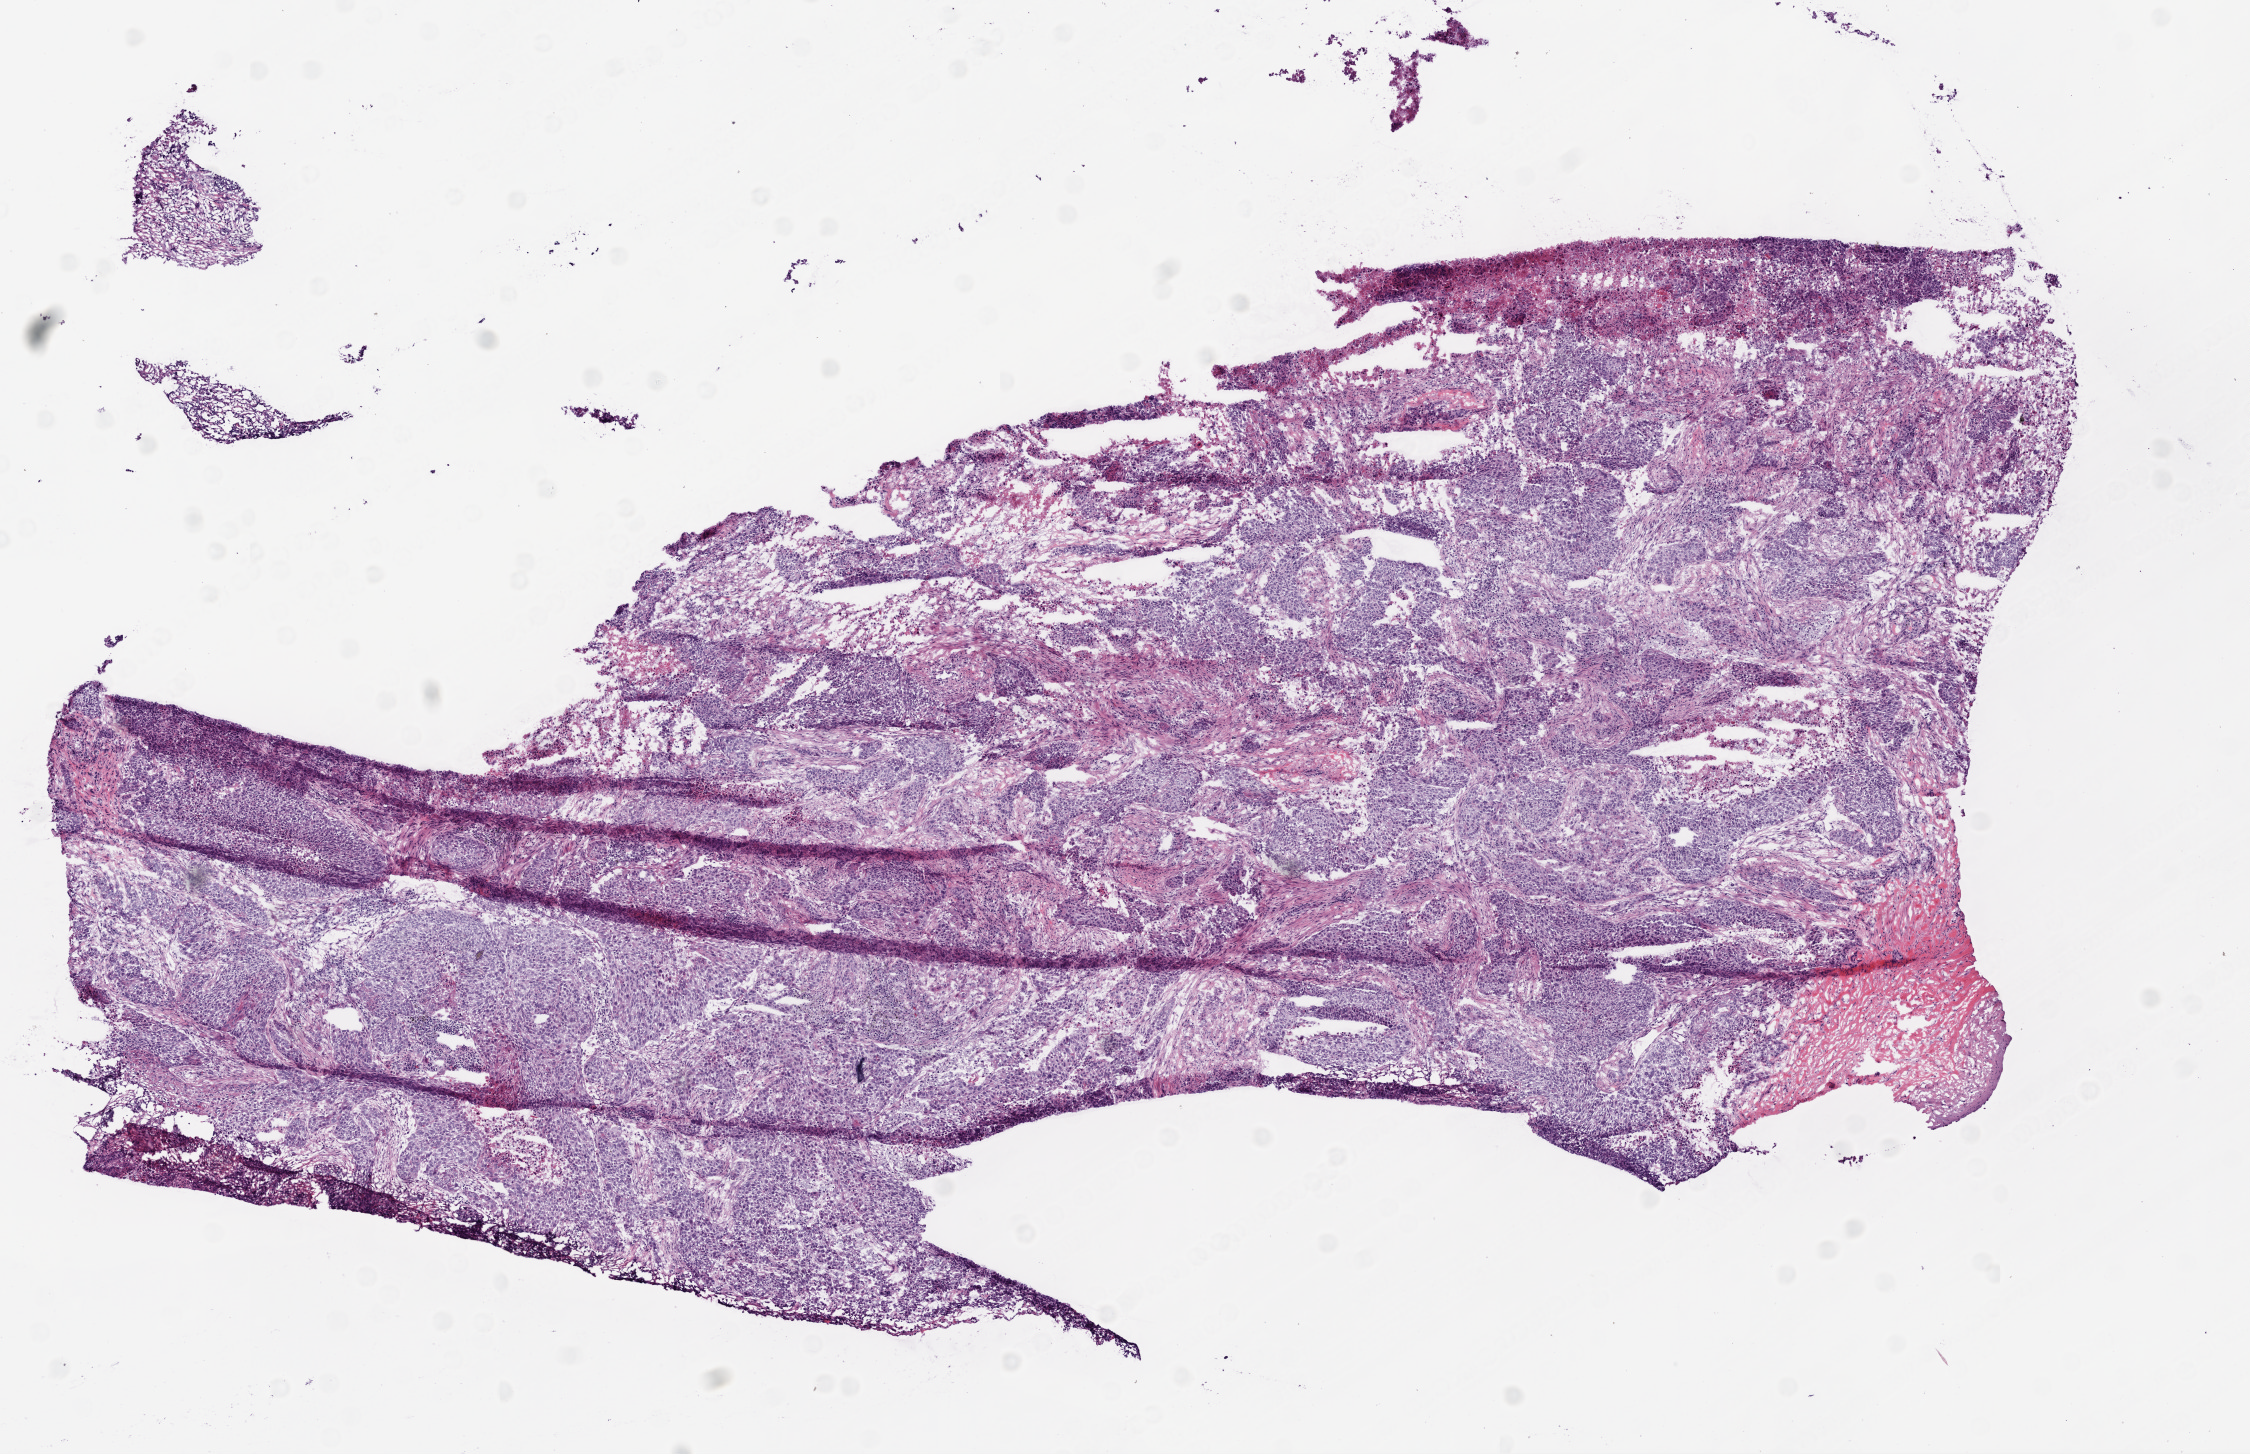
Whole-slide histology image, H&E-stained — shown as a low-resolution overview of the whole scanned area (about 9.0 x 5.8 mm), frozen section from the bottom of the tissue portion, lung, primary tumour sample. Male, age 68 years at initial diagnosis. Composition of this section per pathologist review: tumour cells 85%, tumour nuclei 80%.
Diagnosis: Squamous cell carcinoma, NOS.